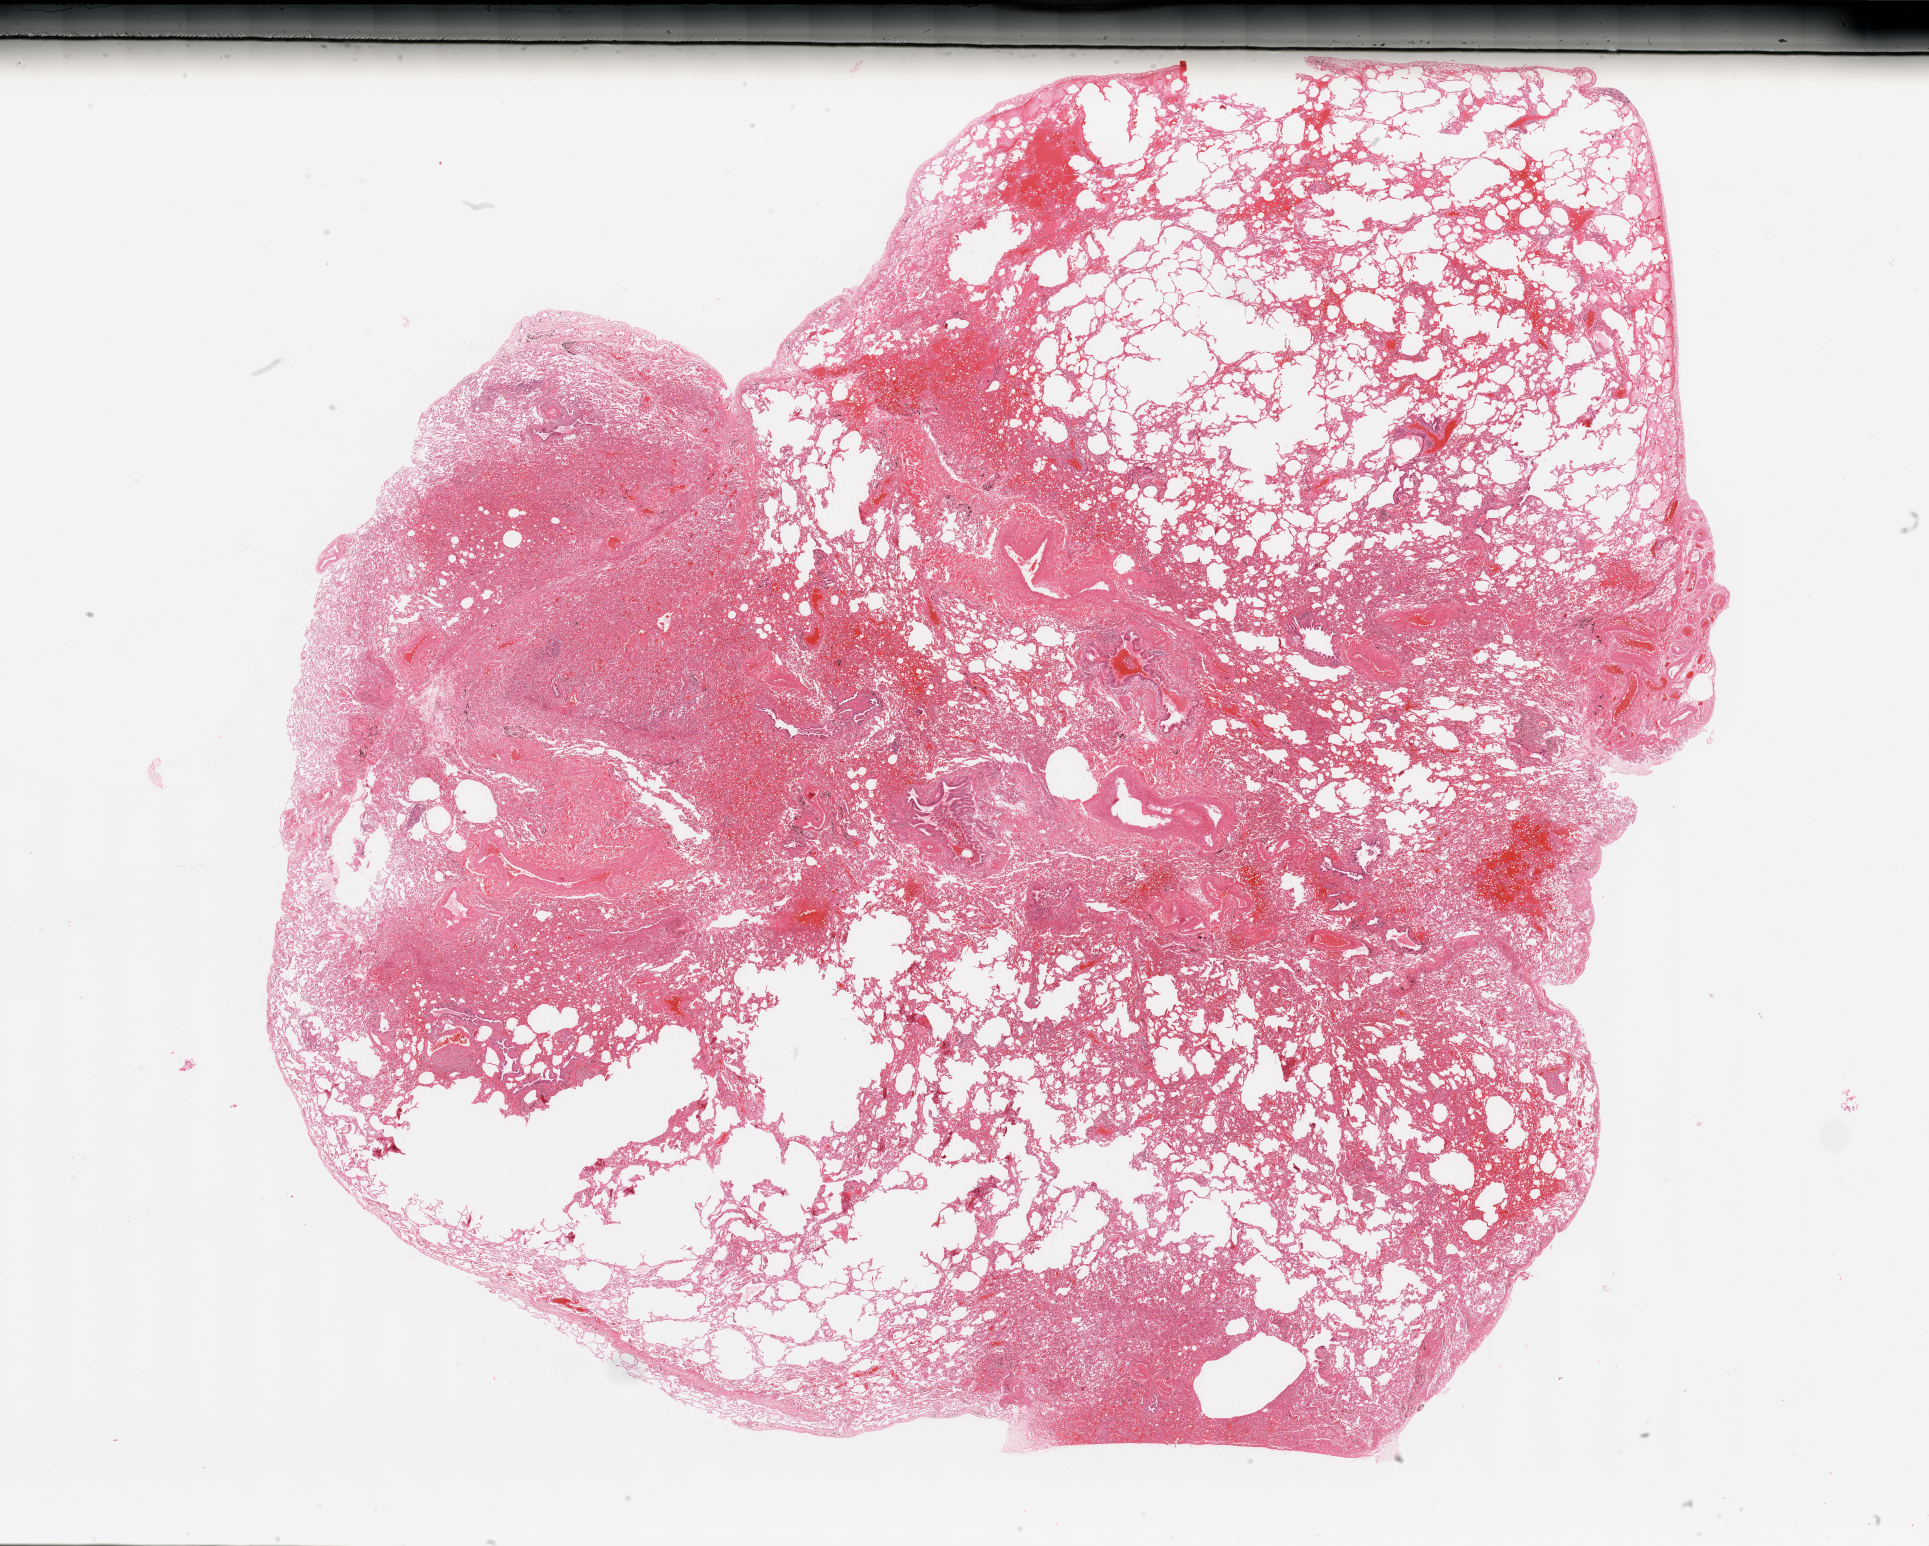
Whole-slide histology image, H&E-stained, low-resolution overview of the scanned area, about 30.5 x 24.5 mm. Lung, normal (non-tumour) tissue. Male, 67 y/o.
* this section: normal (non-tumour) tissue from the same patient
* patient diagnosis: Adenocarcinoma, NOS